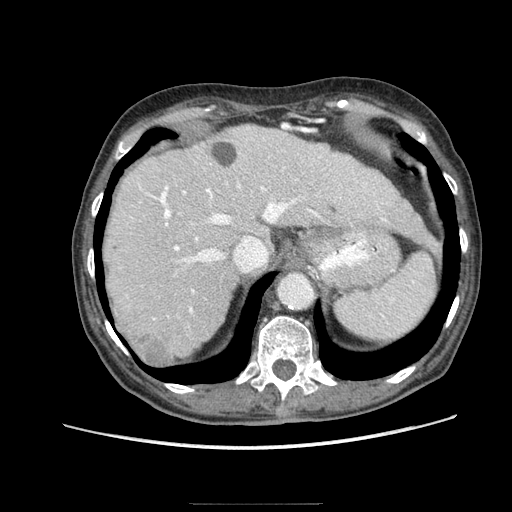
Contrast-enhanced abdominal CT (liver protocol), one axial slice. Slice 64 of 83 in the series (ordered by position). 140 kVp. Soft-tissue window (W 400 / L 40 HU). 512 × 512 image matrix. Case-level facts recorded for this patient, not image findings: diagnosis: hepatocellular carcinoma (patient treated with transarterial chemoembolisation; whether this scan precedes or follows treatment is not stated here); TNM stage (as recorded): Stage-I; Child-Pugh class: A; tumour differentiation: moderately differentiated; tumour nodularity: uninodular.
Annotated regions visible in this slice (semi-automatic segmentation, software-assisted and operator-edited):
- abdominal aorta: box from (x=277, y=273) to (x=315, y=309) px
- liver parenchyma outside the tumour (the mass and vessels are separate outlines, so this box may not span the whole liver): (x=104, y=124)–(x=427, y=358)
- mass: (x=134, y=333)–(x=171, y=367)
- liver vessels: (x=139, y=155)–(x=386, y=320)